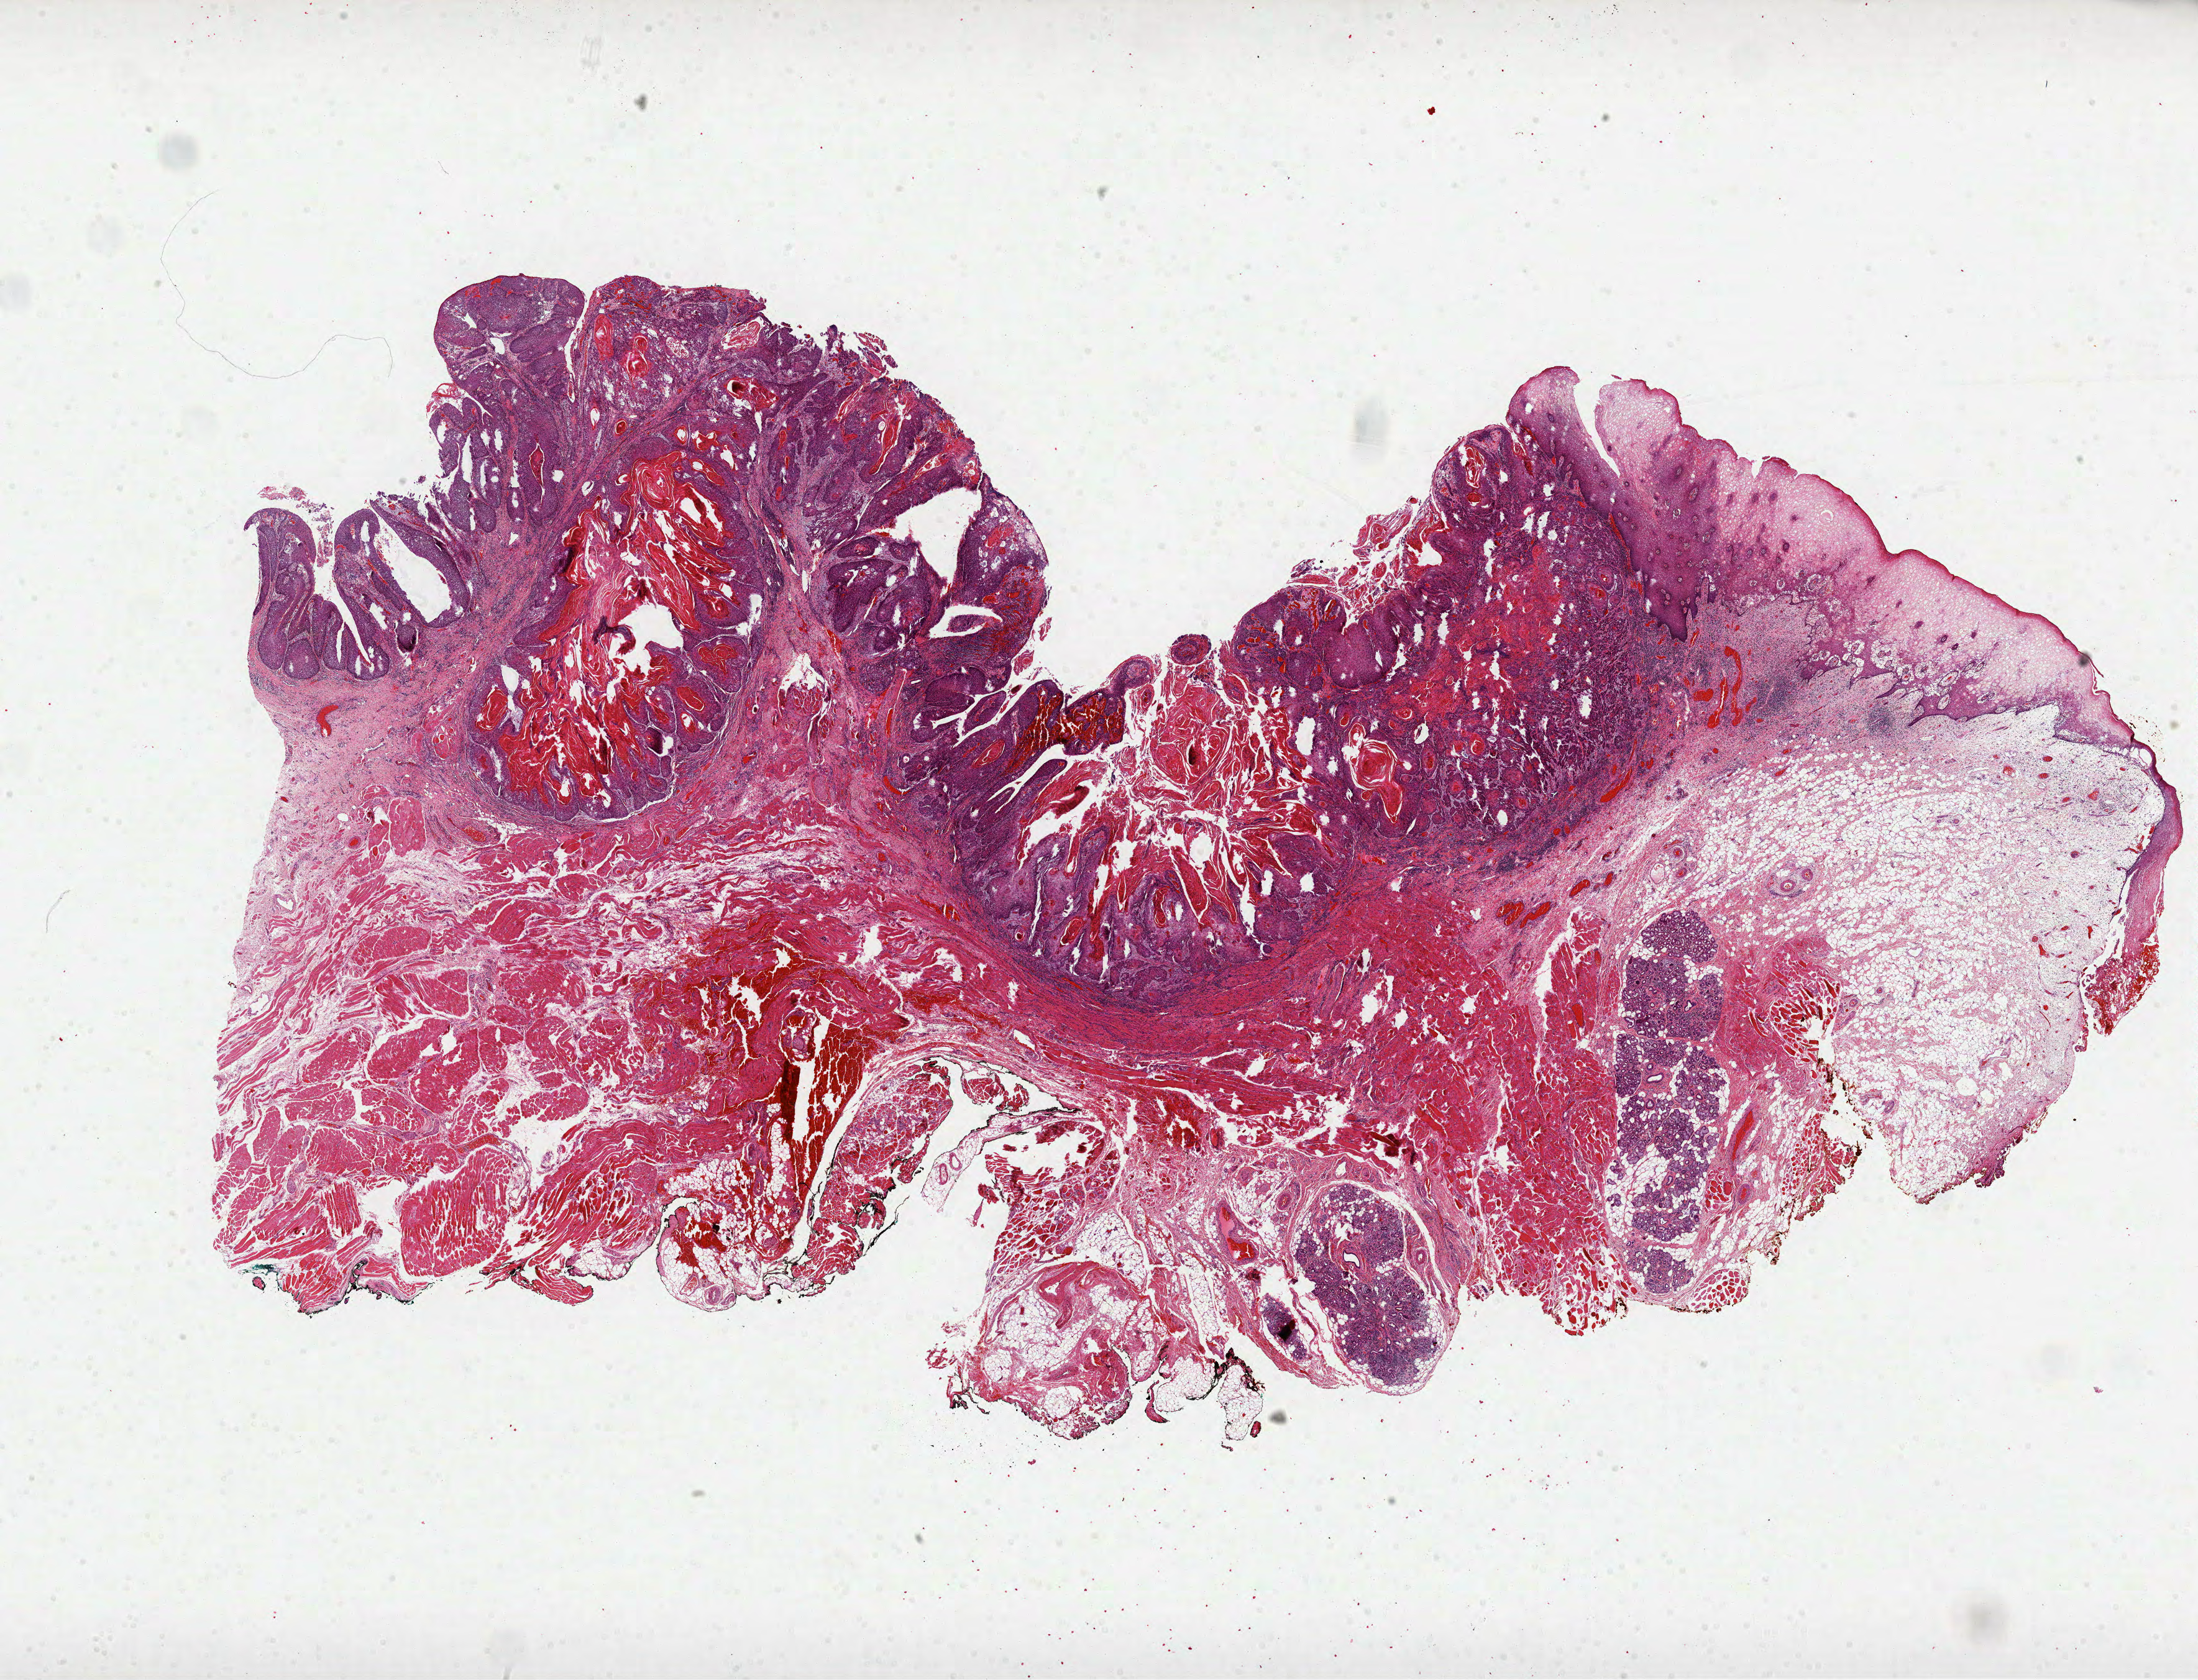
Whole-slide histology image, Hematoxylin and eosin (H&E) stained, whole scanned area (about 28.5 x 21.8 mm) shown as a low-resolution overview; FFPE section; sample: primary tumour, head and neck. Male patient; age at initial diagnosis 62 years. Histologic grade: G1 (well differentiated).
Lymph nodes positive (case pathology): 0 of 13 examined. TNM: T2 N0. AJCC pathologic stage: II (7th edition). Laterality: right. Histologic diagnosis: Squamous cell carcinoma, keratinizing, NOS (floor of mouth, NOS).